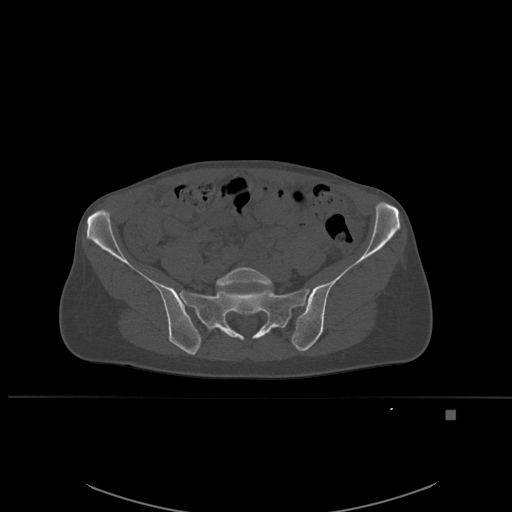
CT including the spine, one axial slice. Slice 159 of 537 in the series (ordered by position). Bone window (W 1800 / L 400 HU). 1.5 mm slice thickness. 512 × 512 image matrix, field of view 440 × 440 mm. Patient: female, 45 years. Case-level facts recorded for this patient, not image findings: primary cancer: lung.
Outlined on this slice (semi-automatically segmented with operator editing):
- L5 vertebra: bounding box (x1, y1, x2, y2) in pixels: (216, 267, 273, 289)